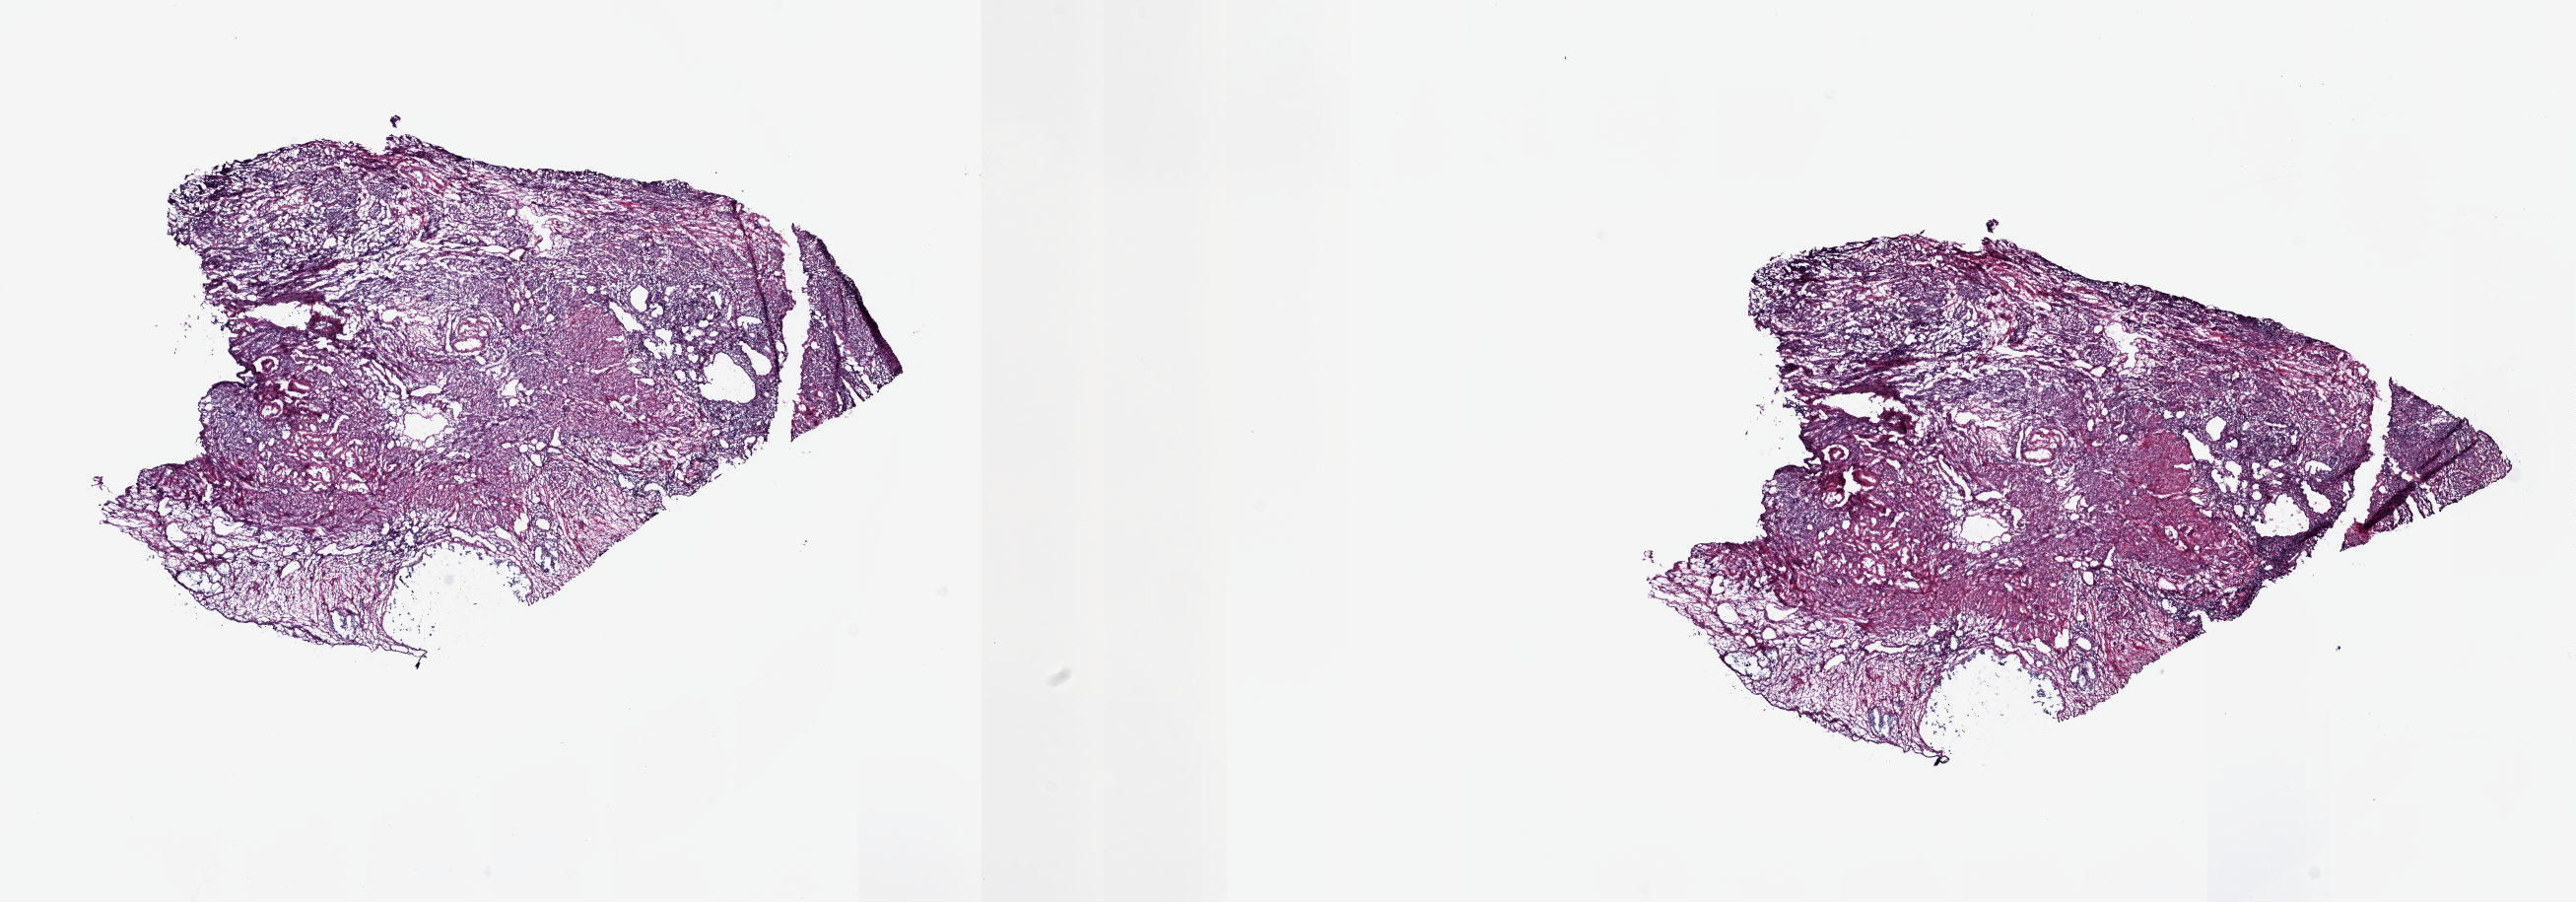
Digitized H&E tissue section (whole slide) — whole scanned area (about 20.8 x 7.3 mm) shown as a low-resolution overview; frozen section from the top of the tissue portion; solid tissue normal (non-tumour tissue) sample from the uterus. Pathologist review of this section (percent, as recorded): tumour cells 0%, normal cells 100%.
- this section: solid tissue normal (non-tumour) sample